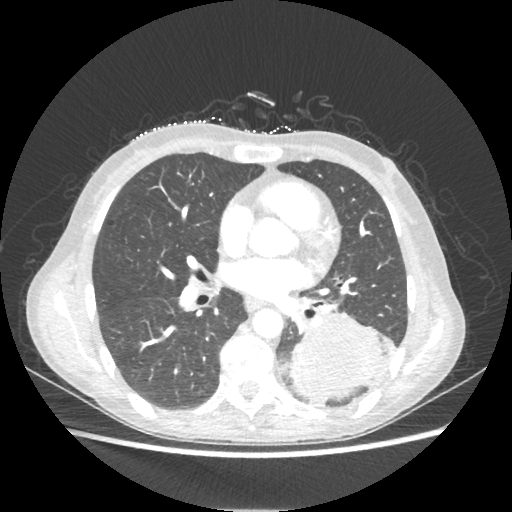
Chest CT, one axial slice; slice 107 of 221 in the series (ordered by position); 80 kVp; lung window (W 1500 / L -600 HU); 1.25 mm slice thickness; 512 × 512 image matrix. Patient: female, 53 years. From the clinical record (not read from this slice): clinical TNM (as recorded): T3 N0 M0.
Annotated regions visible in this slice (rectangle marked by the reading radiologist):
- lung tumour (recorded histology: adenocarcinoma): bounding box <290,311,381,406> (left, top, right, bottom; pixels)